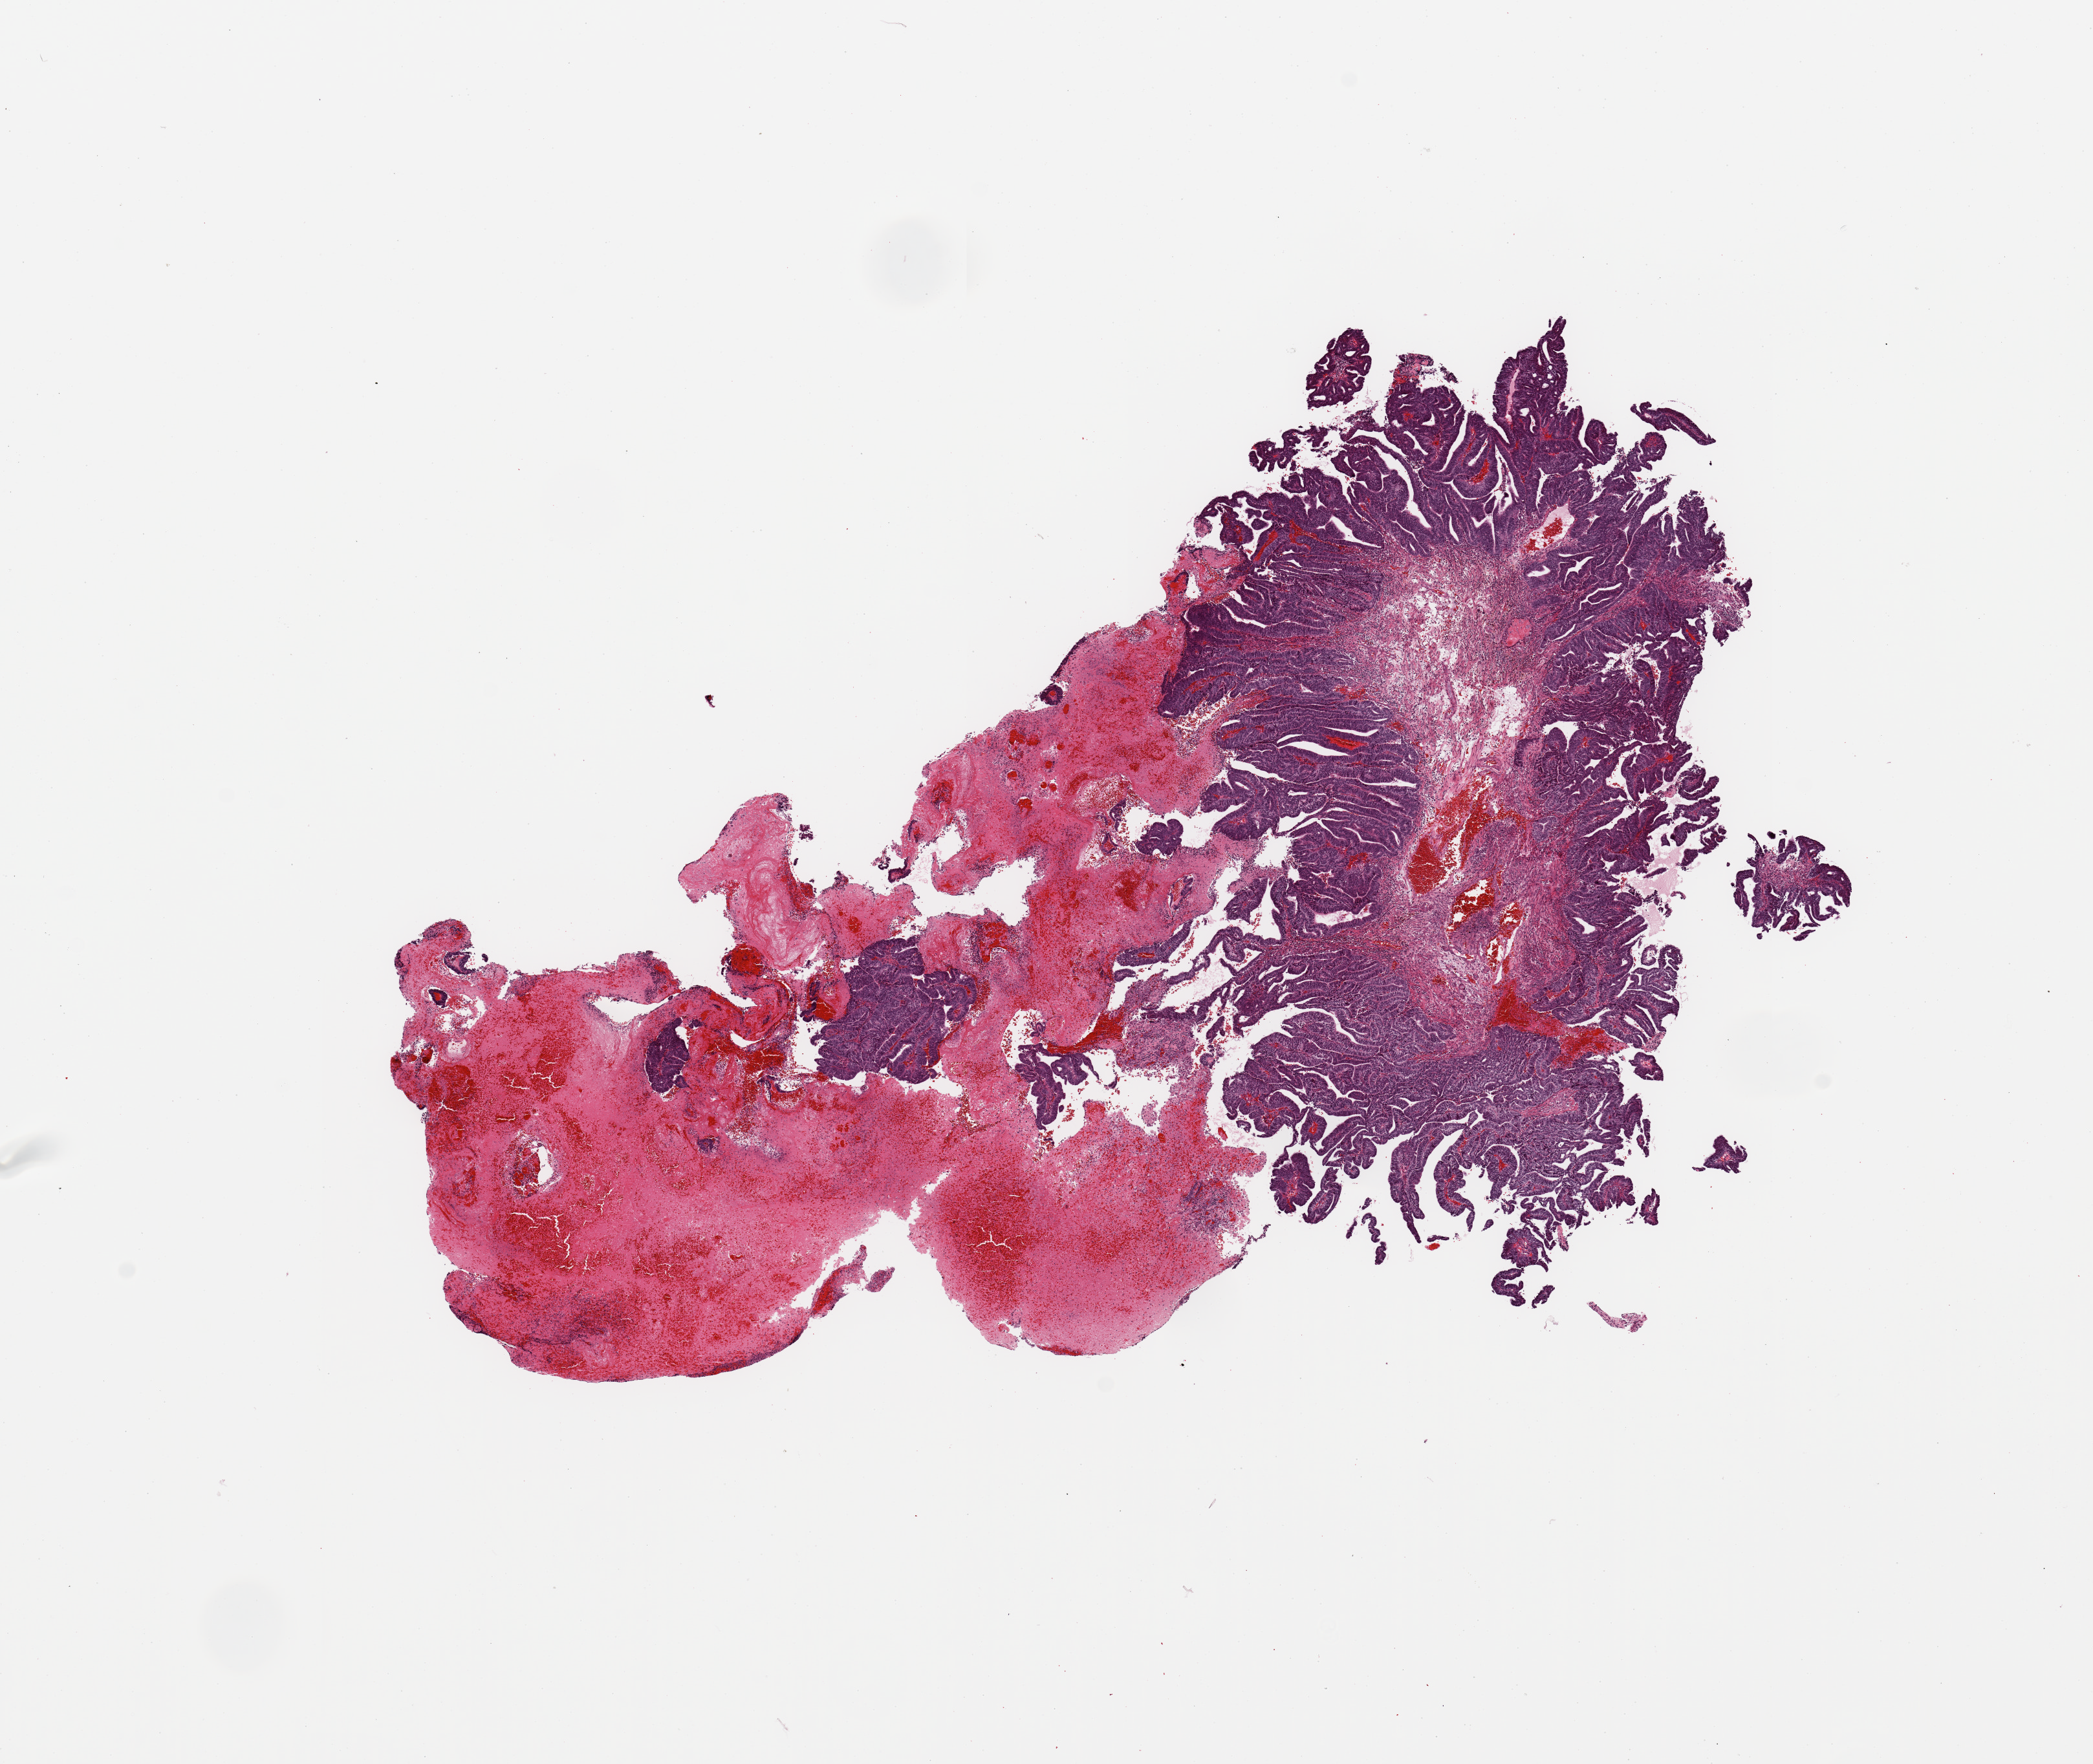
Whole-slide histology image, H&E-stained, whole scanned area (about 12.8 x 10.8 mm, acquisition: 20x scan) shown as a low-resolution overview; uterus, tumour tissue. Patient: female, age 57 years. Histologic grade: G1 (well differentiated).
* histologic diagnosis: Endometrioid adenocarcinoma, NOS
* AJCC pathologic stage: I